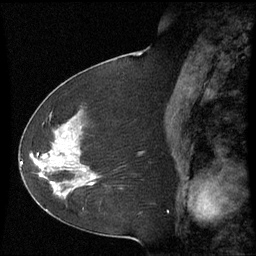
Breast MRI (dynamic contrast-enhanced), one sagittal slice. Slice 29 of 60 in the series (ordered by position). Dynamic contrast-enhanced series, image 2 of 3 at this slice position (ordered by acquisition). 1.5 T. TE 4.2 ms, TR 8.9 ms. 2.3 mm slice thickness. 256 × 256 image matrix, field of view 210 × 210 mm. Female patient, age 51 years. From the clinical record (not read from this slice): setting: breast cancer imaged before/during neoadjuvant chemotherapy; receptor status: HR-positive, HER2-negative.
Outlined on this slice (semi-automatic segmentation, software-assisted and operator-edited):
- analysis volume of interest (the breast-tissue region the enhancement analysis was run in; not a lesion): bounding box (x1, y1, x2, y2) in pixels: (50, 117, 102, 187)
- tumour enhancement mask (voxels above the 70 % enhancement threshold inside the analysis volume of interest): (84, 170, 93, 186)